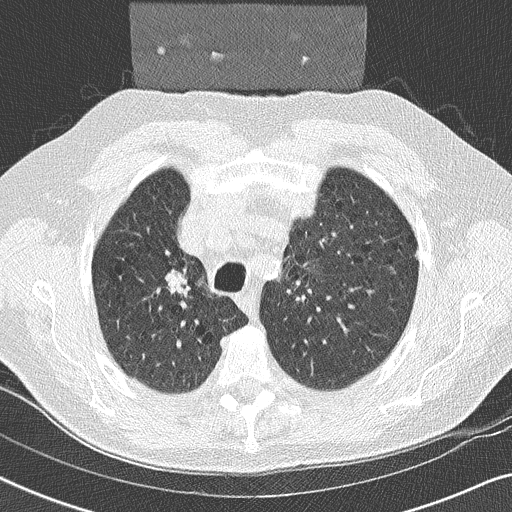
Chest CT (low-dose screening protocol), one axial image; second annual screen; lung window (W 1500 / L -600 HU); lung (sharp) reconstruction kernel (B50f); 512 × 512 image matrix, field of view 330 × 330 mm. Male participant, aged 59 years at enrolment. Former smoker at enrolment.
Lesion marked by an expert reader, bounding box (x1, y1, x2, y2) in pixels: (153, 260, 208, 308). The exam's reader record, not a measurement of the box and not confirmed to be the same lesion: non-calcified nodule or mass ≥4 mm, right upper lobe, 17 × 16 mm, smooth margins, soft tissue attenuation, pre-existing on the prior screen: yes. Official screen result: positive, other. Later outcome: lung cancer diagnosed 14 days after this screen — squamous cell carcinoma, NOS, right upper lobe, poorly differentiated (G3), stage IIA (AJCC 6th edition), 20 mm at pathology.